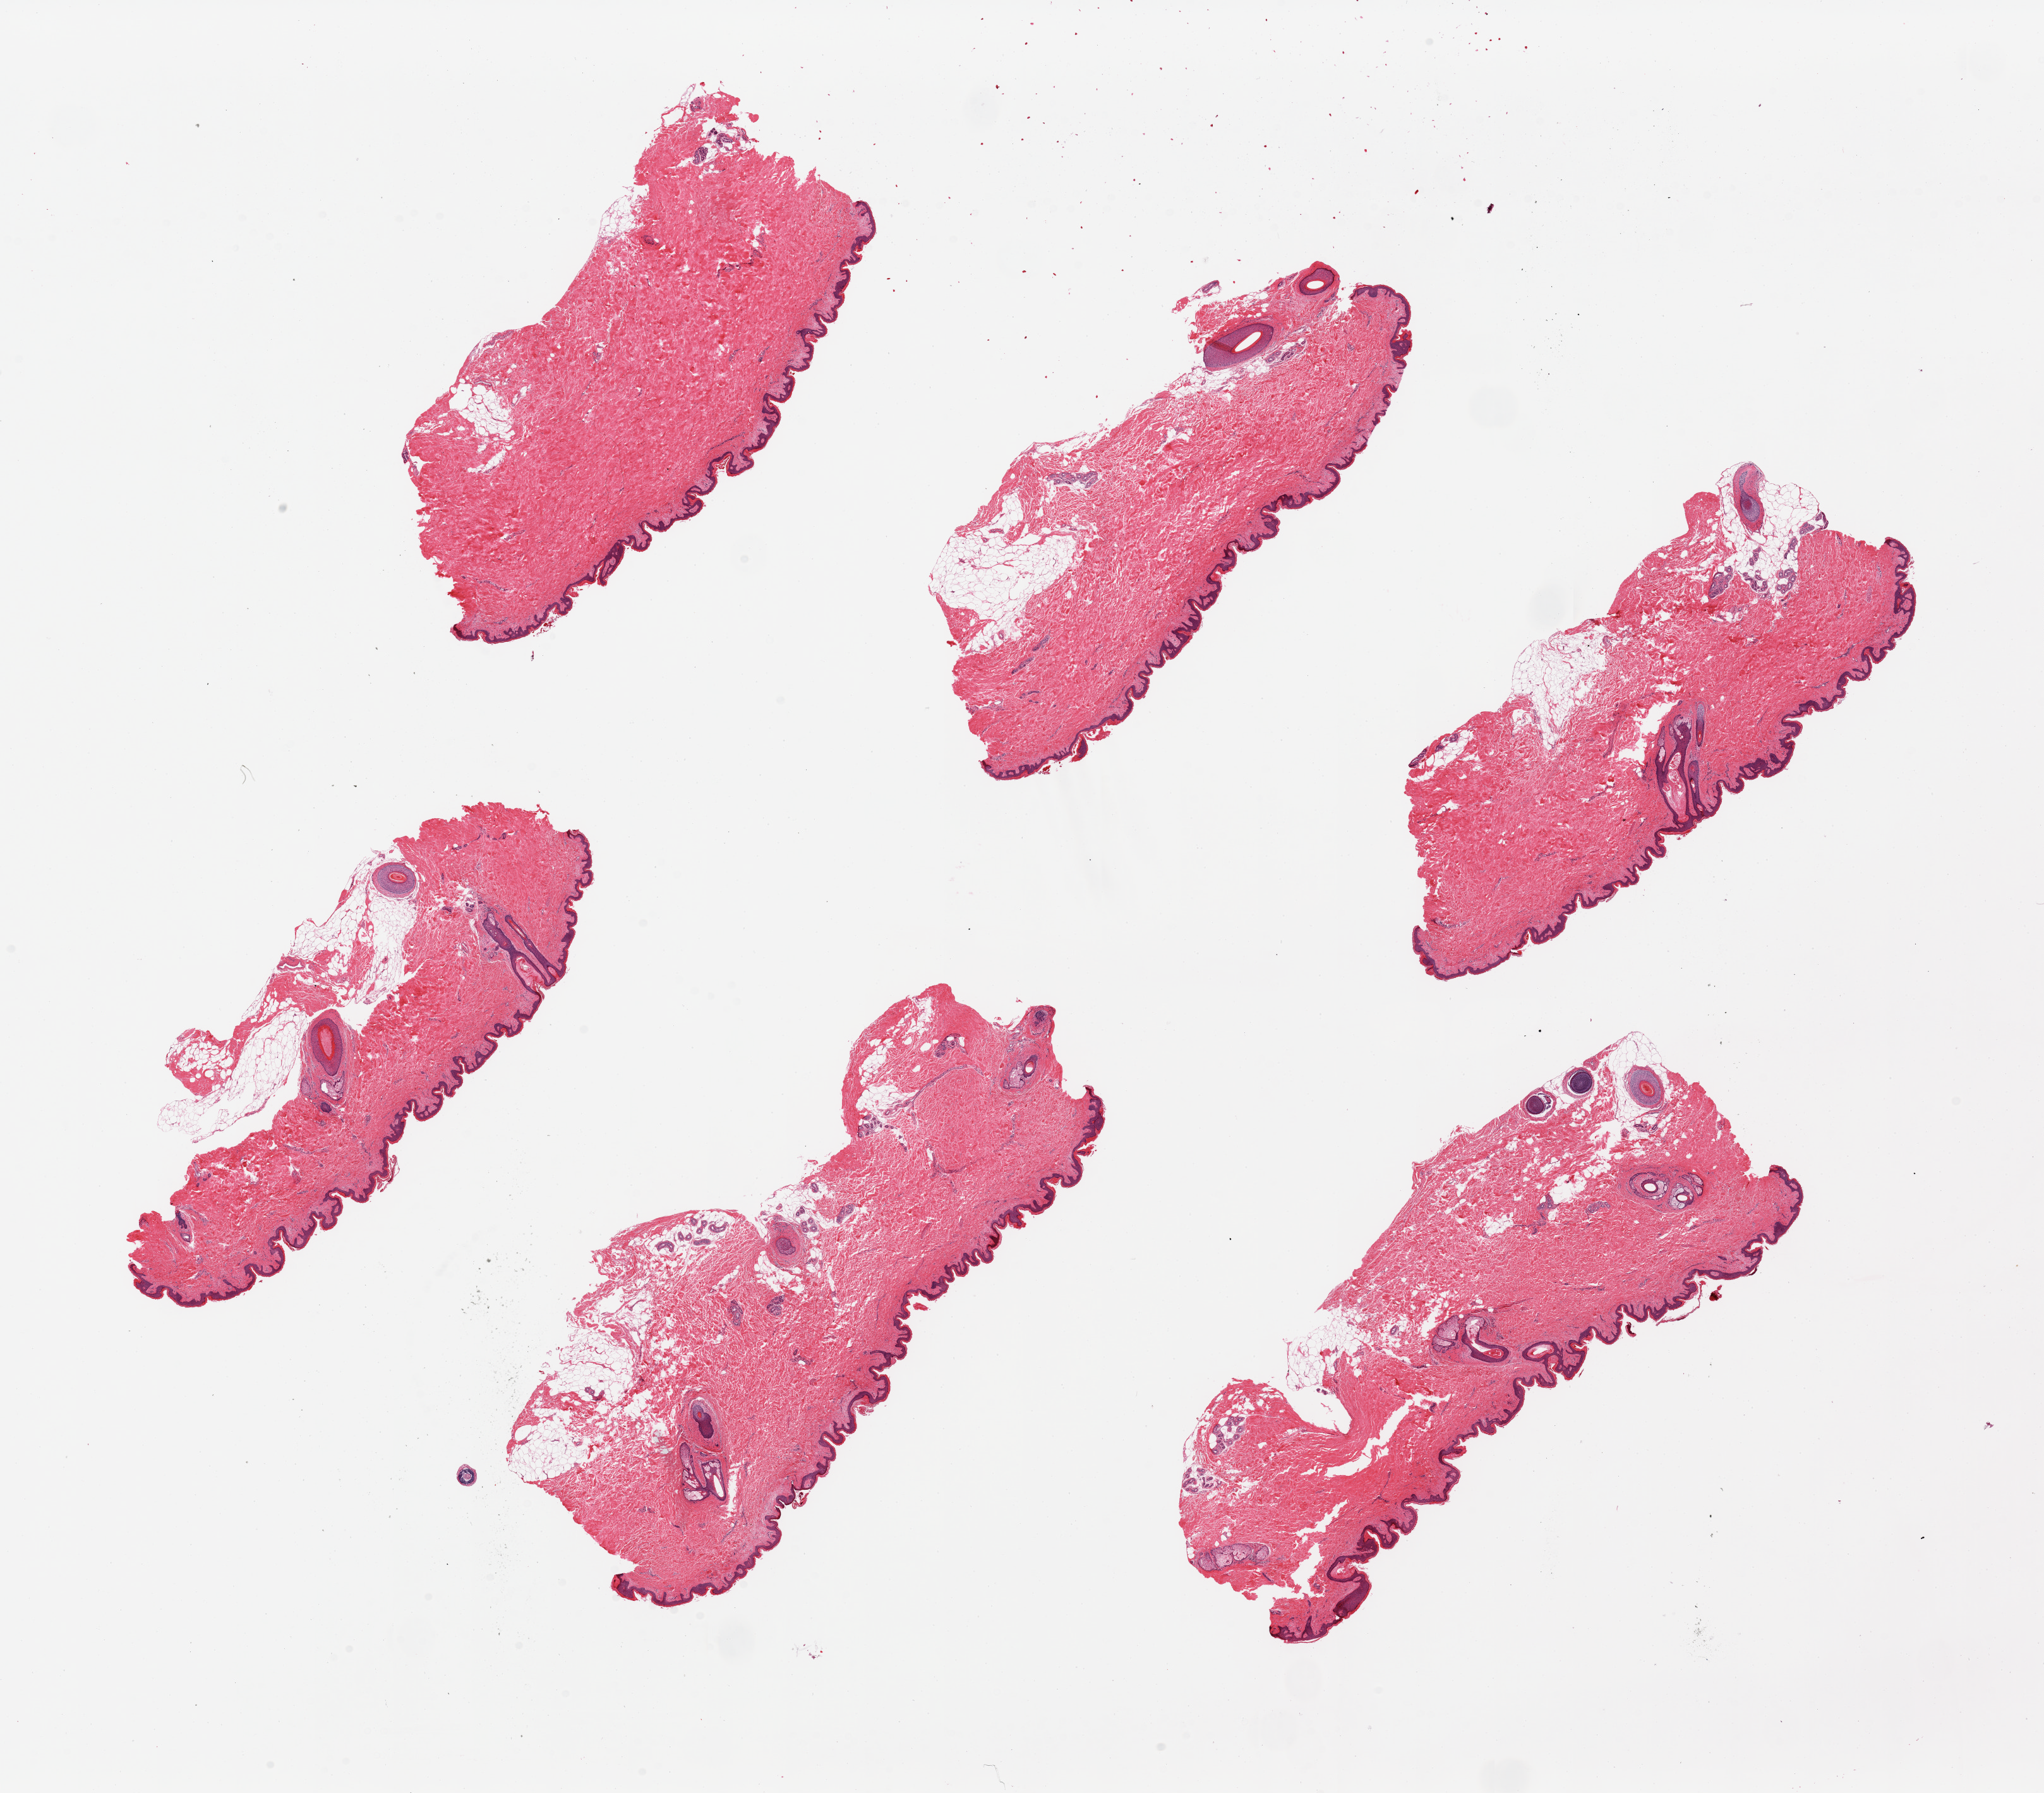
Haematoxylin and eosin whole-slide image — whole scanned area (about 25.6 x 22.4 mm, acquisition: 20x scan) shown as a low-resolution overview; PAXgene-fixed, paraffin-embedded tissue; section of skin of suprapubic region (target tissue); donor tissue sample.
* review note (as recorded): 3 pieces. Up to 1.3 mm subcutaneous fat on several pieces